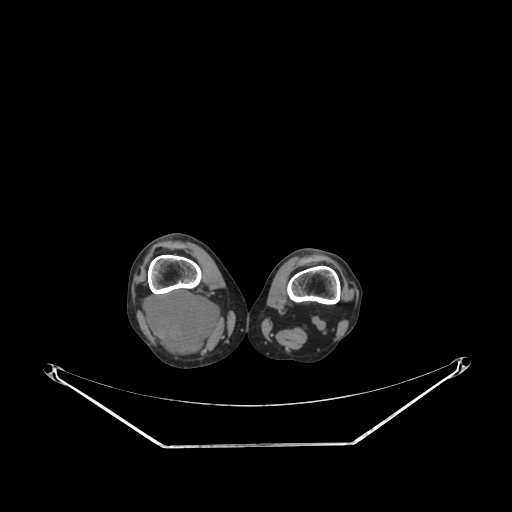
CT of an extremity soft-tissue mass (from a PET/CT study), one axial slice. Reconstruction kernel SOFT. Soft-tissue window (W 400 / L 40 HU). 3.75 mm slice thickness. 512 × 512 image matrix. Female patient. Case-level facts recorded for this patient, not image findings: histological type: liposarcoma; site of the primary tumour: right thigh.
Annotated regions visible in this slice (expert contour drawn on MRI and transferred to this co-registered scan by the dataset authors):
- gross tumour volume (mass): bounding box <144,290,222,357> (left, top, right, bottom; pixels)